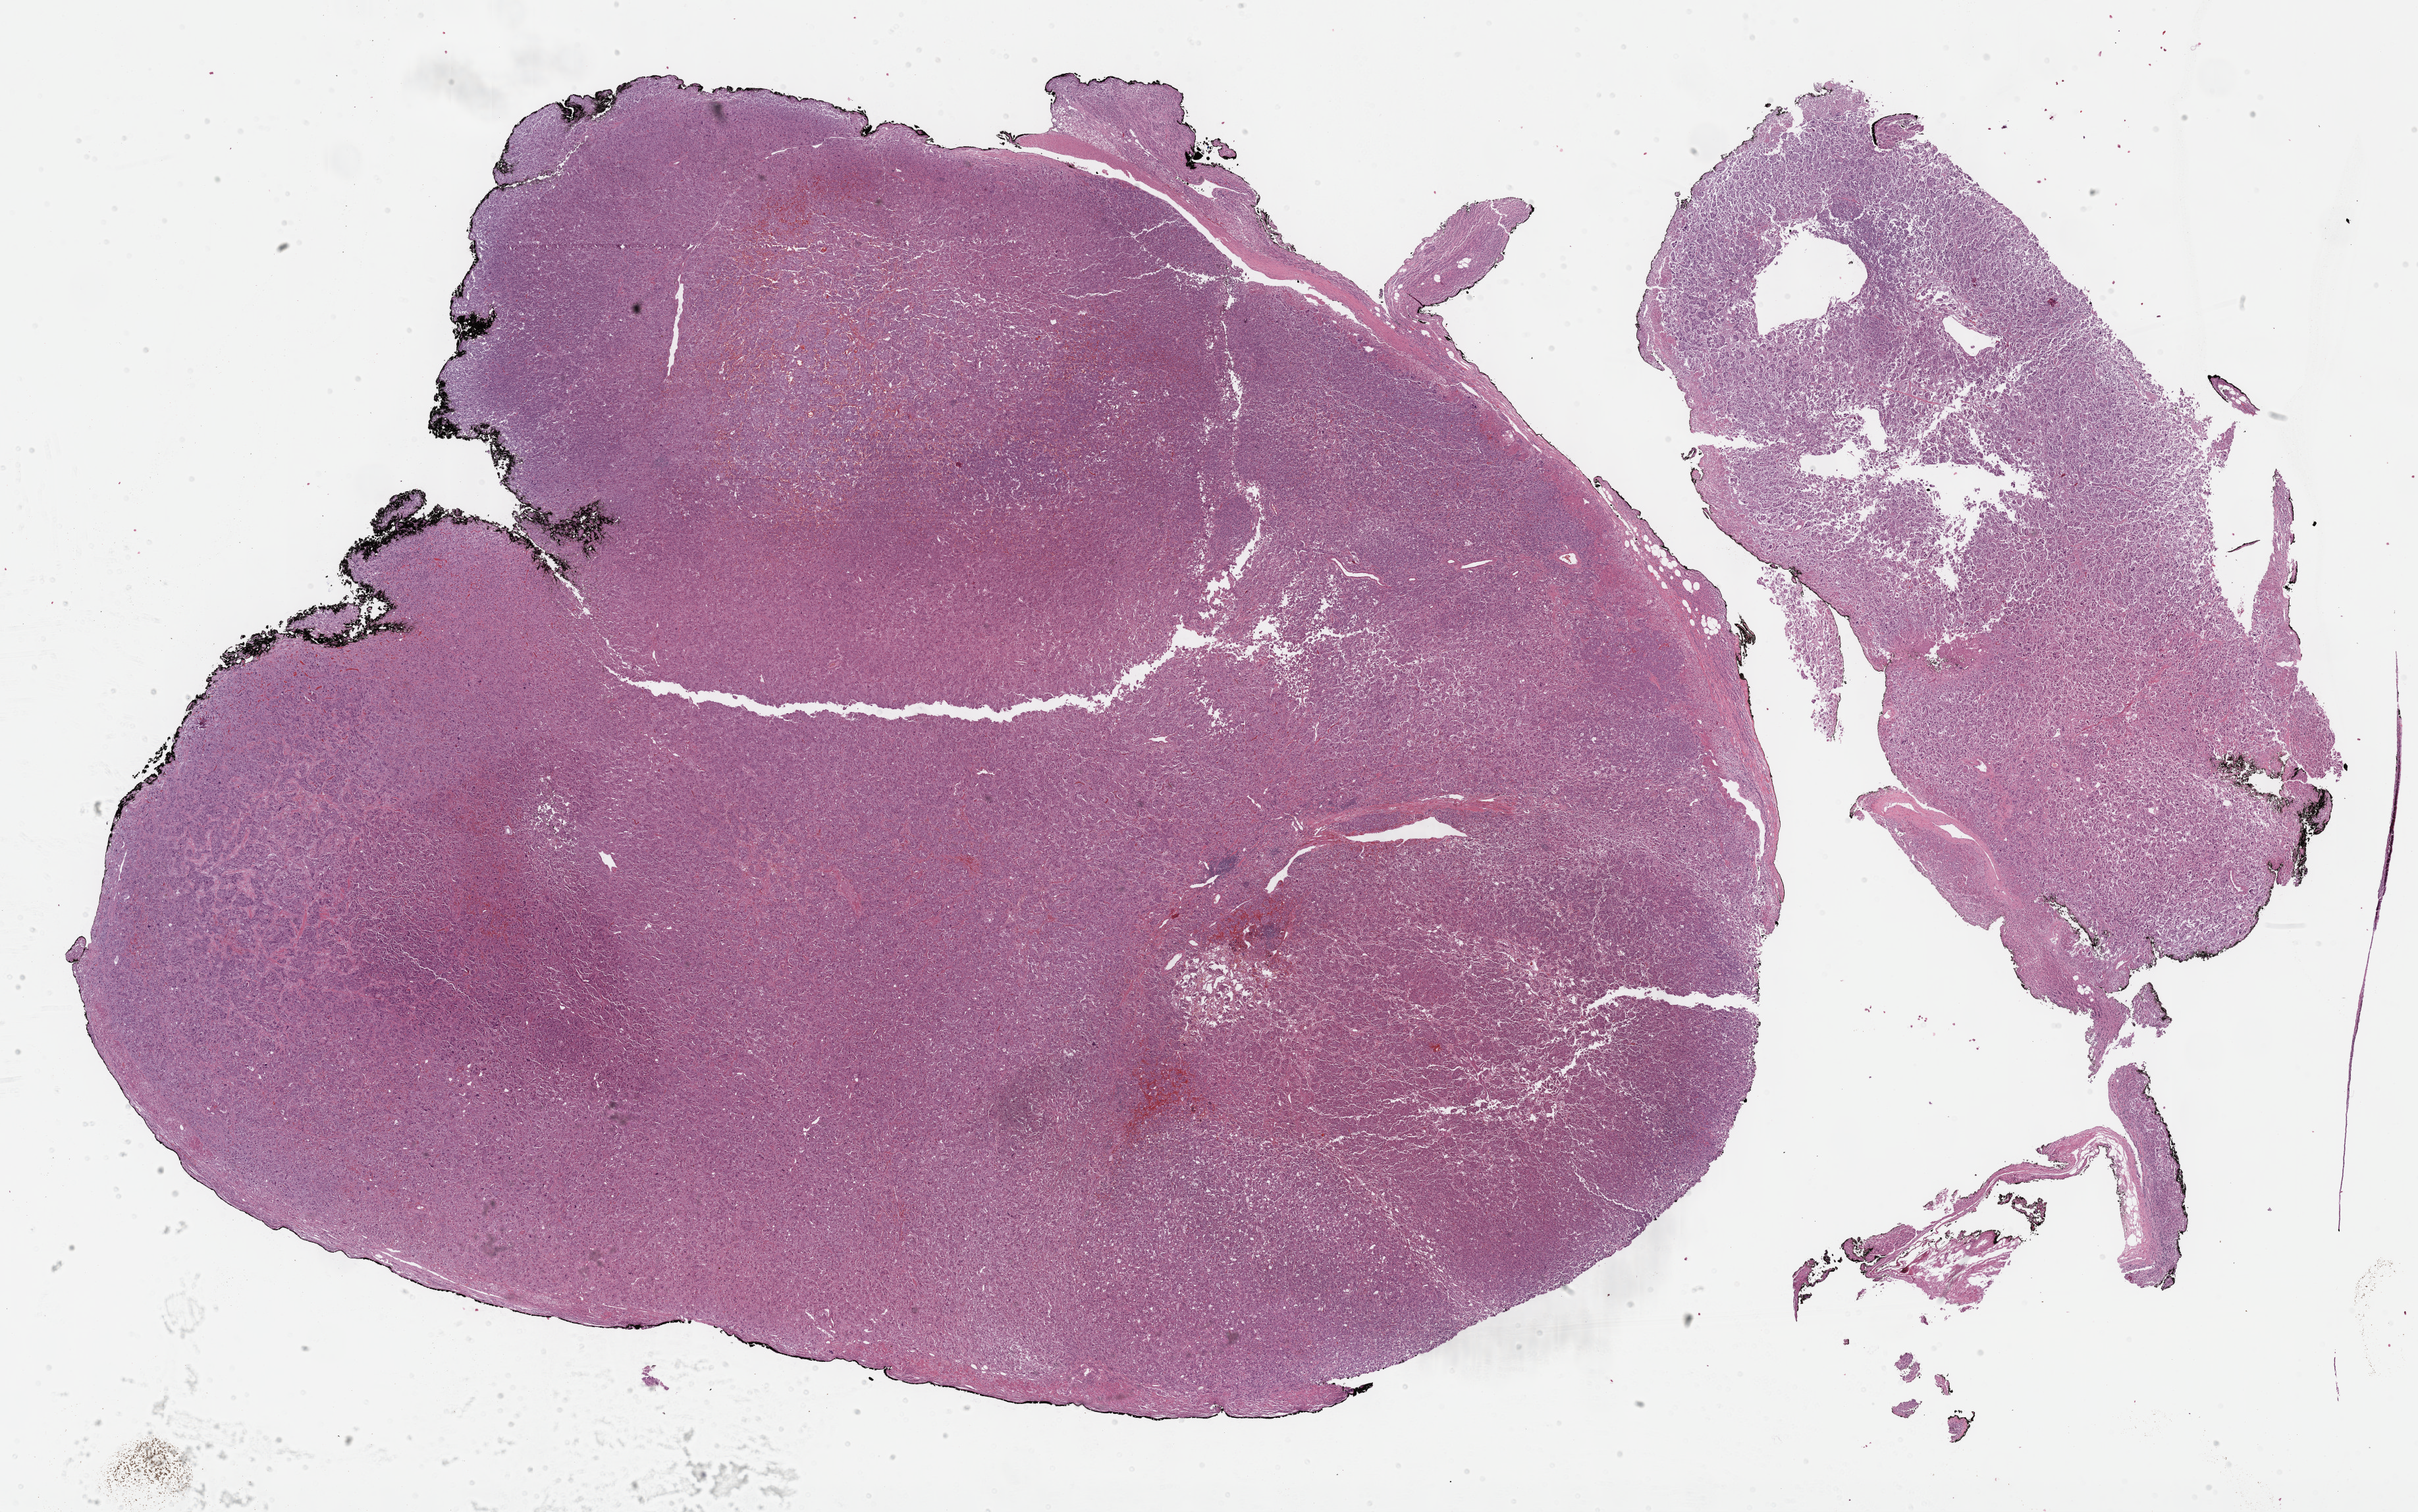
Whole-slide histology image, H&E, whole scanned area (about 29.7 x 18.6 mm) shown as a low-resolution overview. FFPE section. Primary tumour sample from the adrenal gland. Patient: male, age at initial diagnosis 58 years.
- diagnosis: Pheochromocytoma, NOS